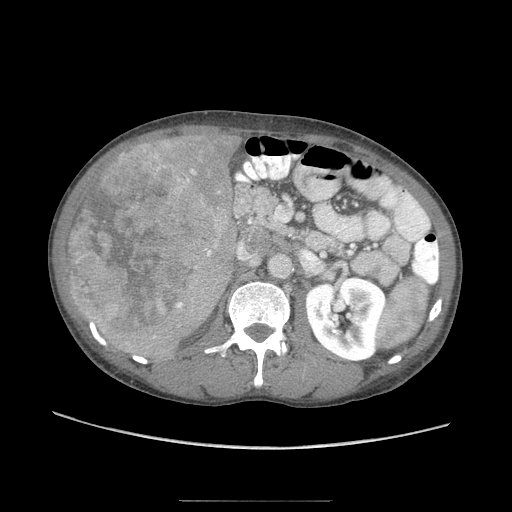
Contrast-enhanced abdominal CT (liver protocol), one axial slice. Slice 33 of 103 in the series (ordered by position). 120 kVp. Soft-tissue window (W 400 / L 40 HU). 512 × 512 image matrix. From the clinical record (not read from this slice): diagnosis: hepatocellular carcinoma (patient treated with transarterial chemoembolisation; whether this scan precedes or follows treatment is not stated here); TNM stage (as recorded): Stage-IIIA; Child-Pugh class: A; tumour differentiation: moderately differentiated.
Structures marked on this image (semi-automatically segmented with operator editing):
- liver parenchyma outside the tumour (the mass and vessels are separate outlines, so this box may not span the whole liver): bounding box [x1, y1, x2, y2] px = [70, 130, 240, 350]
- mass: [65, 140, 220, 344]